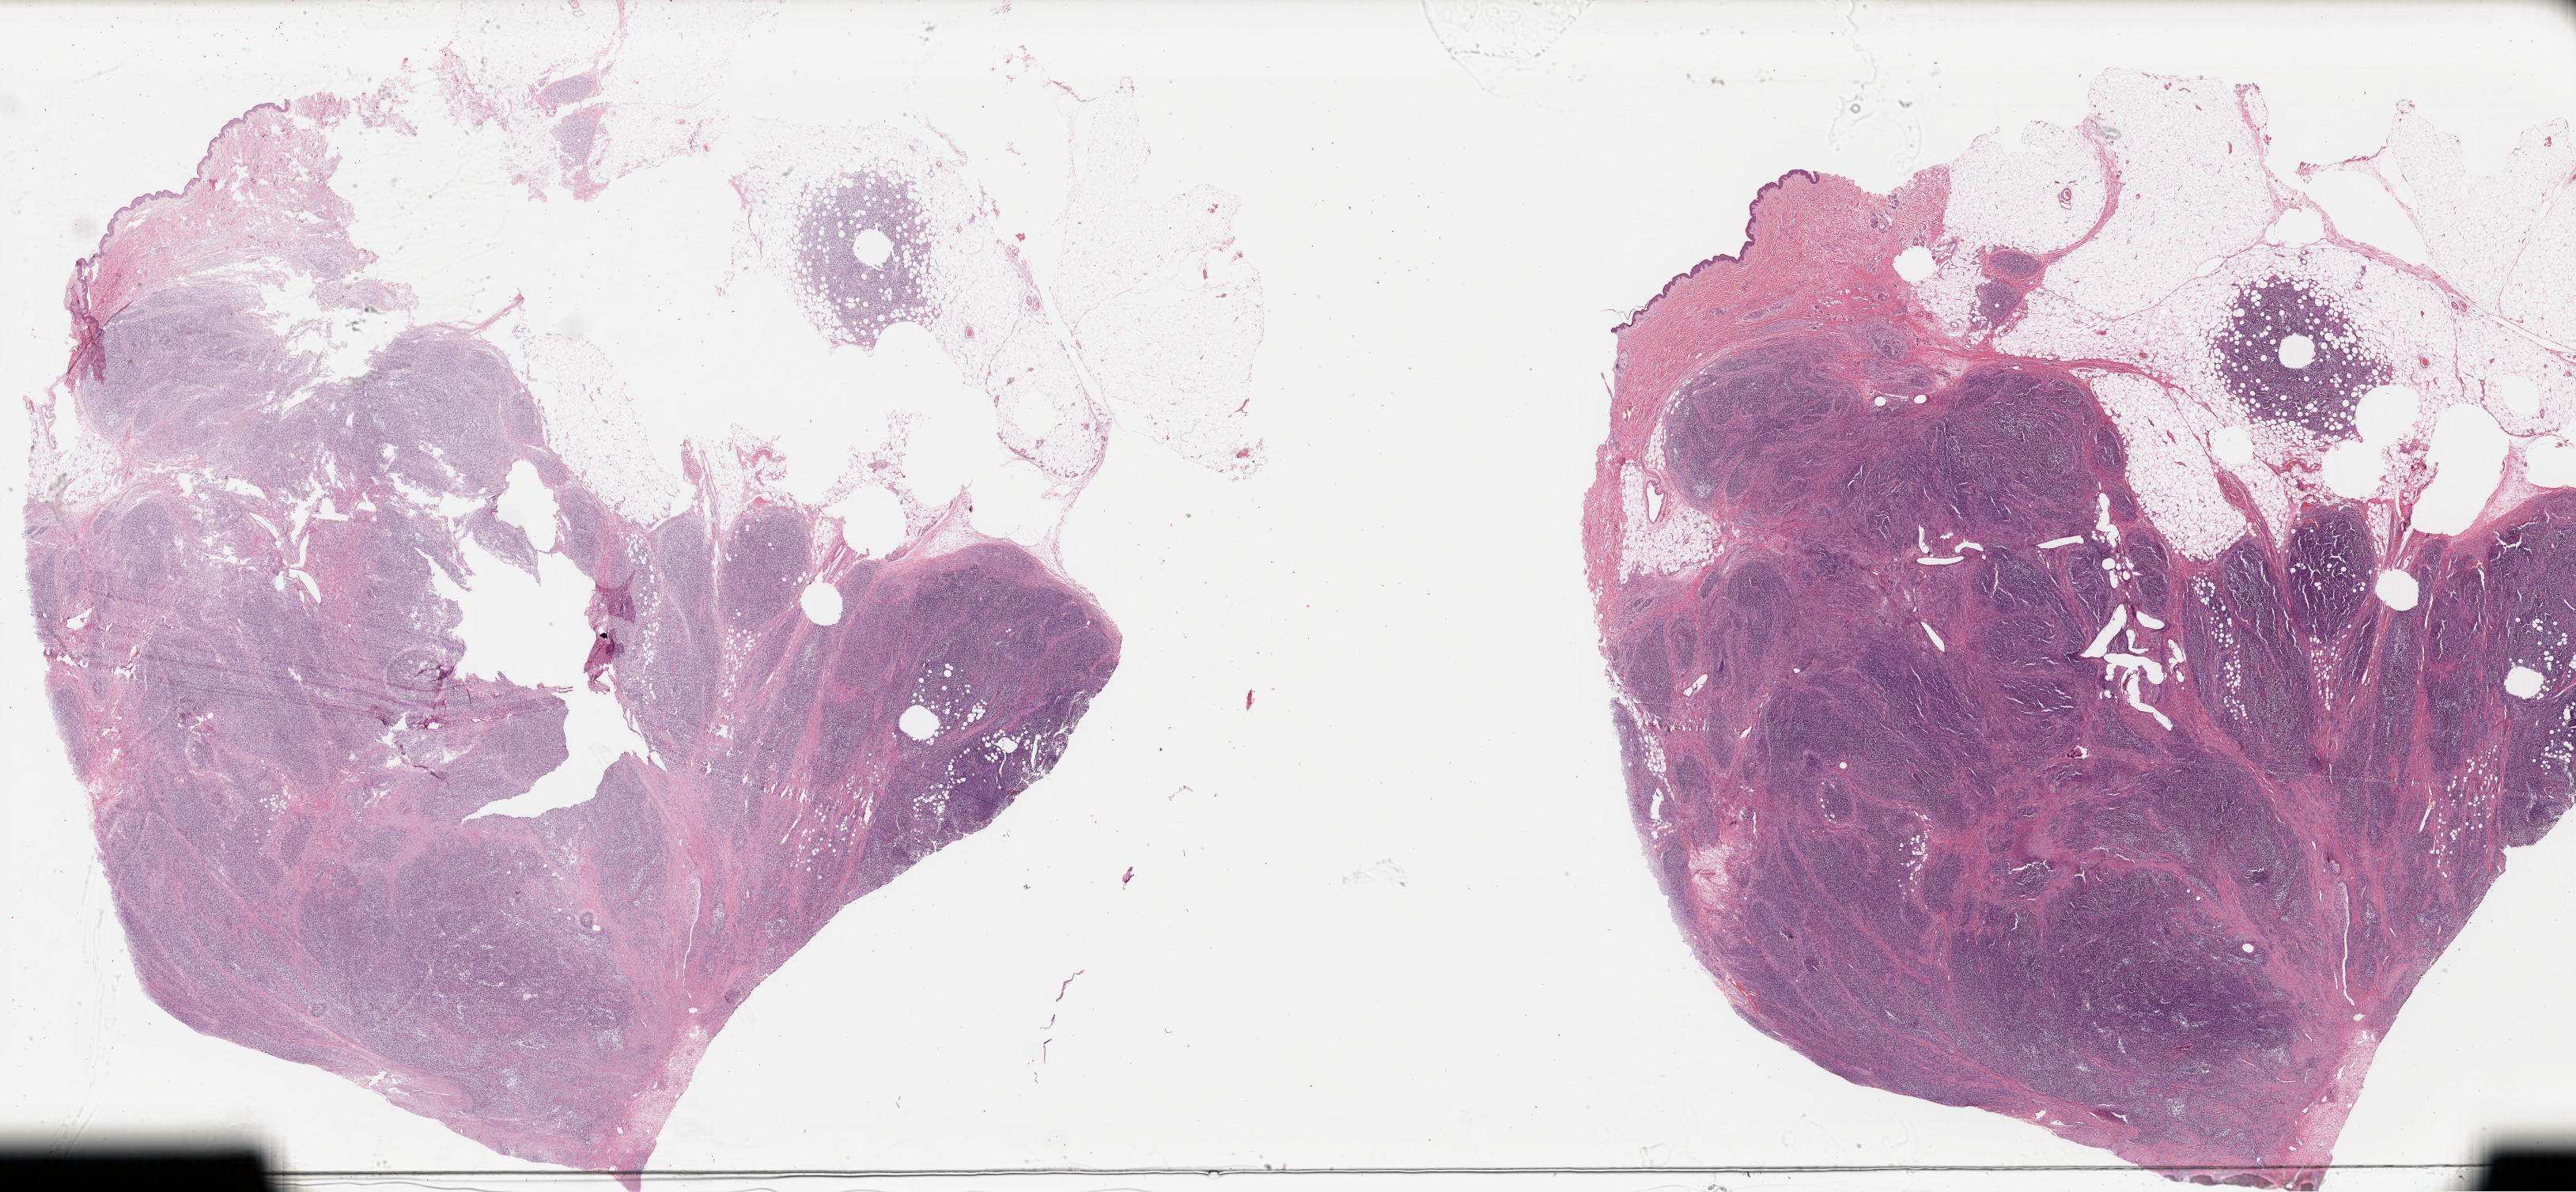
Hematoxylin and eosin (H&E) stained whole-slide image, low-resolution overview of the scanned area, about 51.2 x 23.7 mm (acquisition: 40x scan), formalin-fixed paraffin-embedded (FFPE) diagnostic section, metastatic tumour sample, sampled site: lymph node. Male, age 63 years at initial diagnosis.
This section: metastatic tumour tissue. Patient diagnosis: Malignant melanoma, NOS.